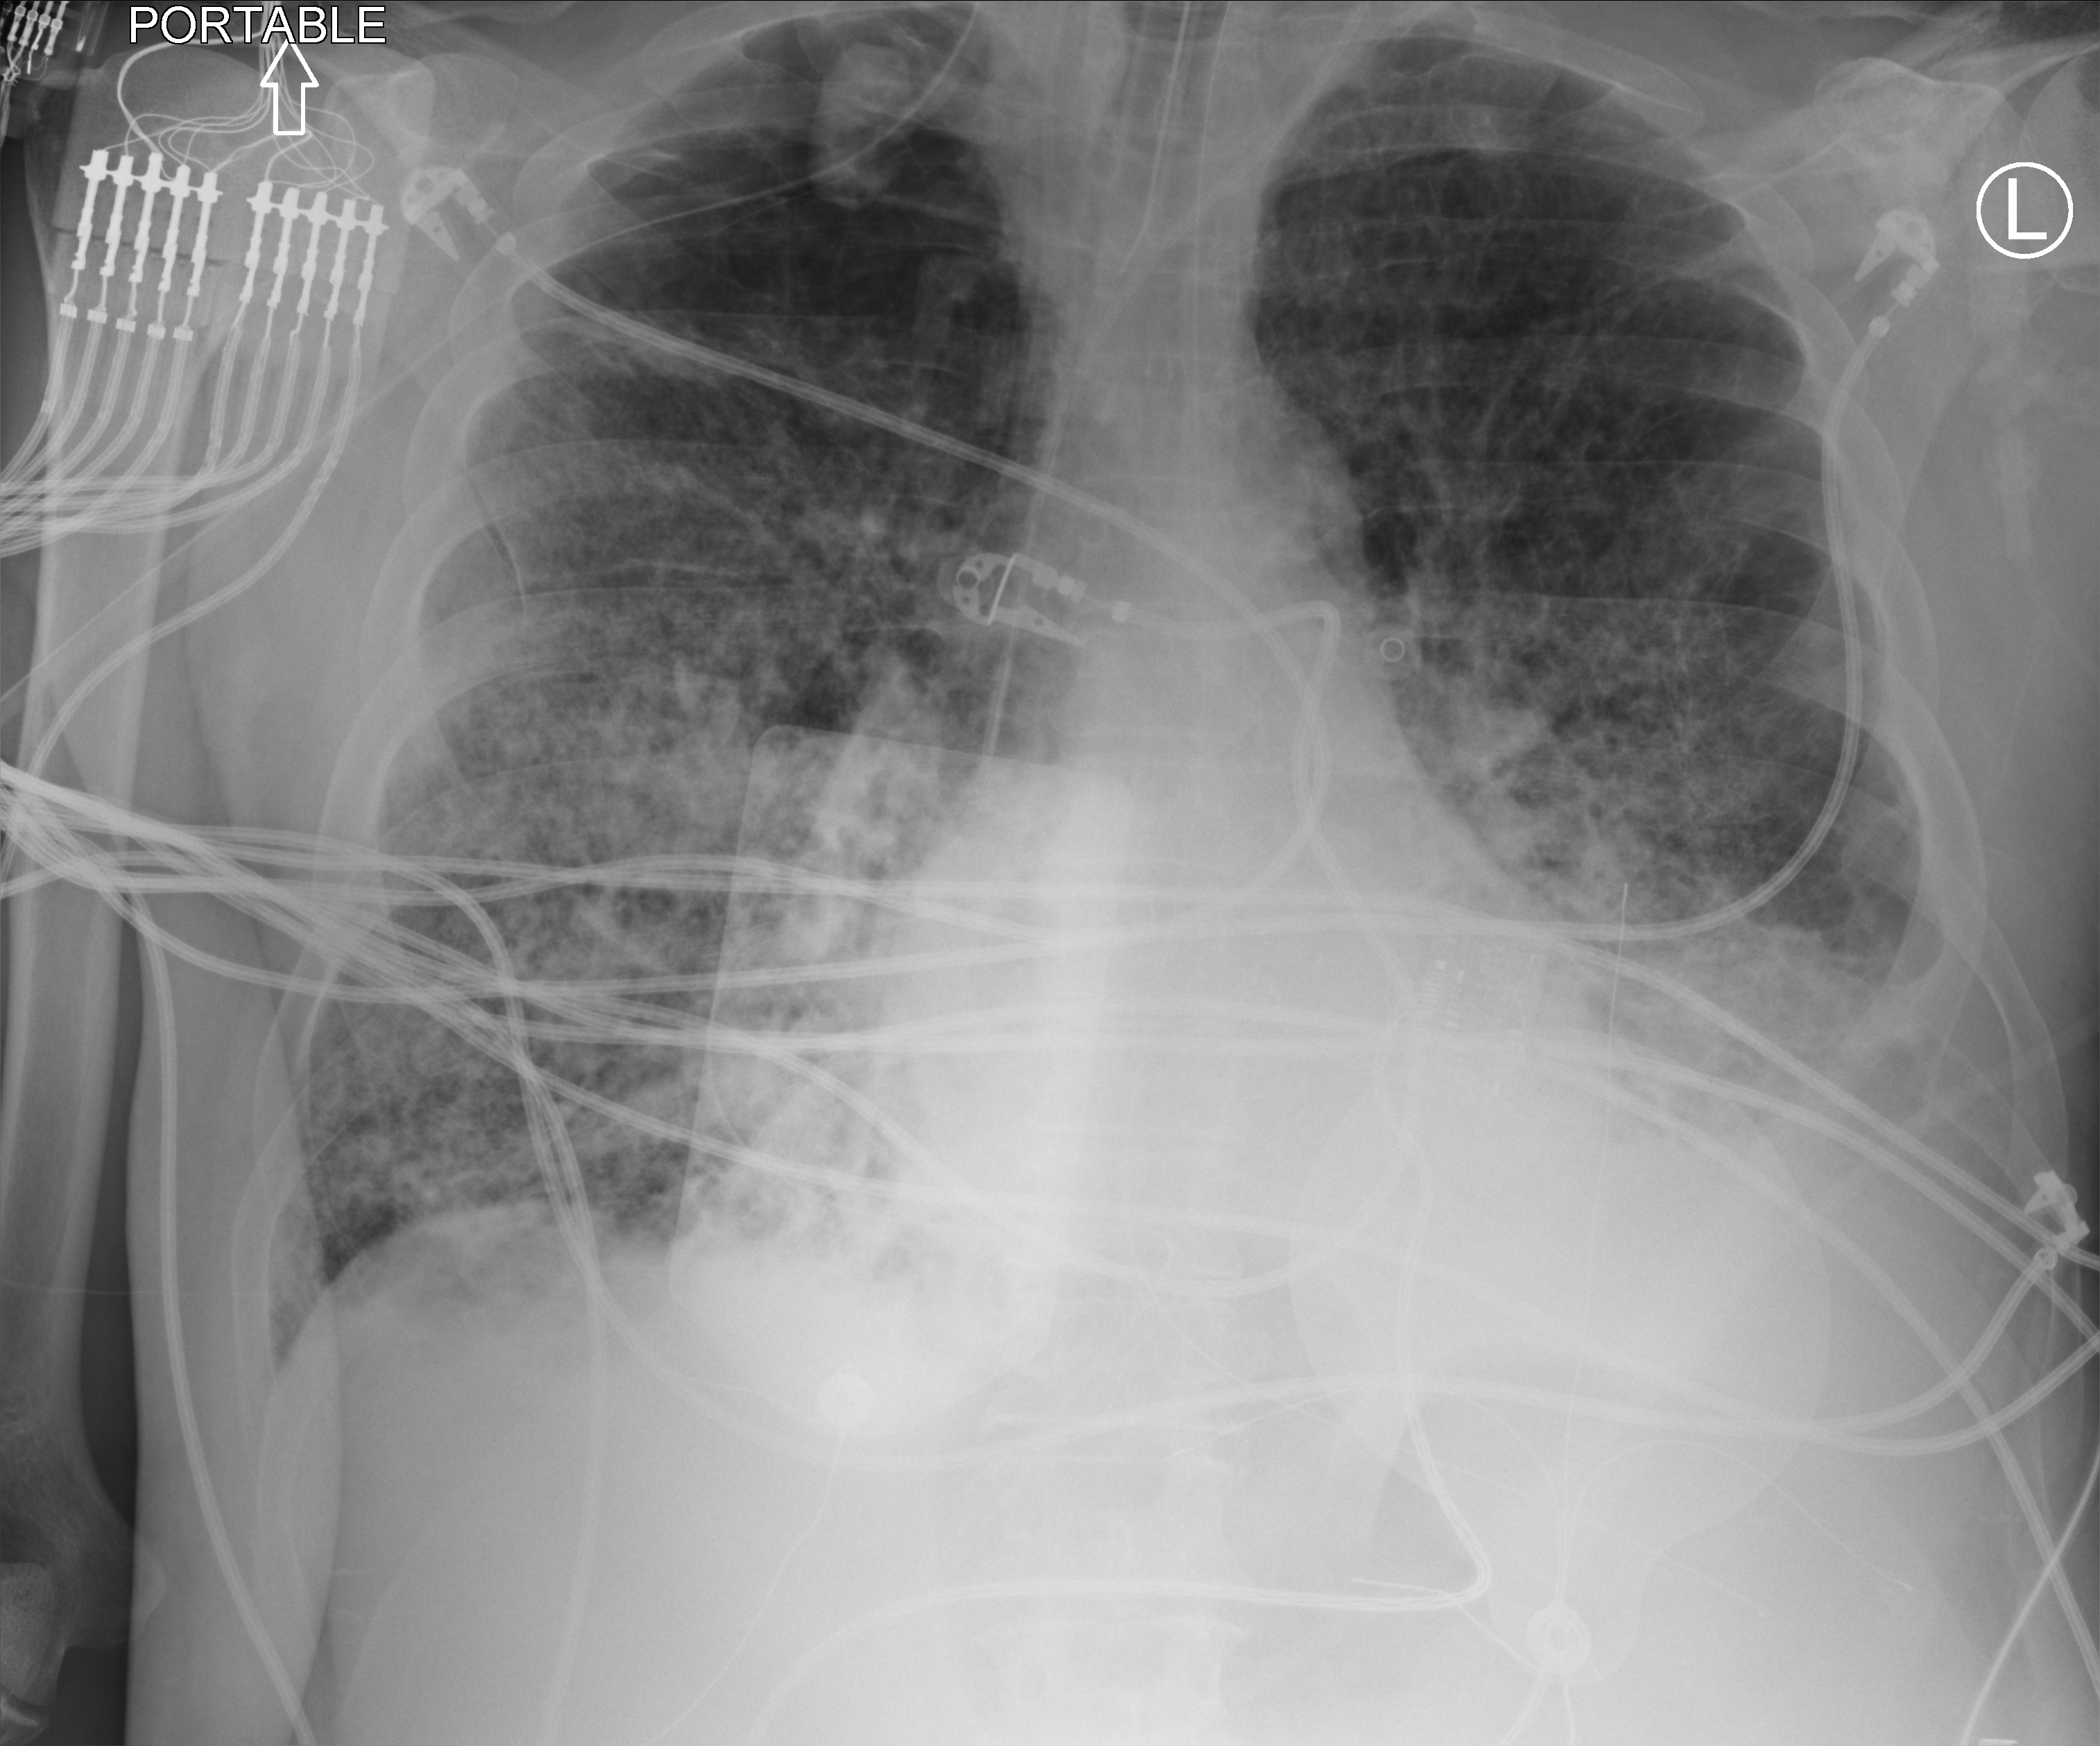
Bedside chest radiograph (computed radiography). Male patient hospitalised with COVID-19, age 75–90 years.
Hospital-stay facts (about this admission, not read from this image; timing relative to this image not recorded): length of hospital stay: 13 days; COPD (admission record): no; admitted to intensive care during this hospital stay: yes.